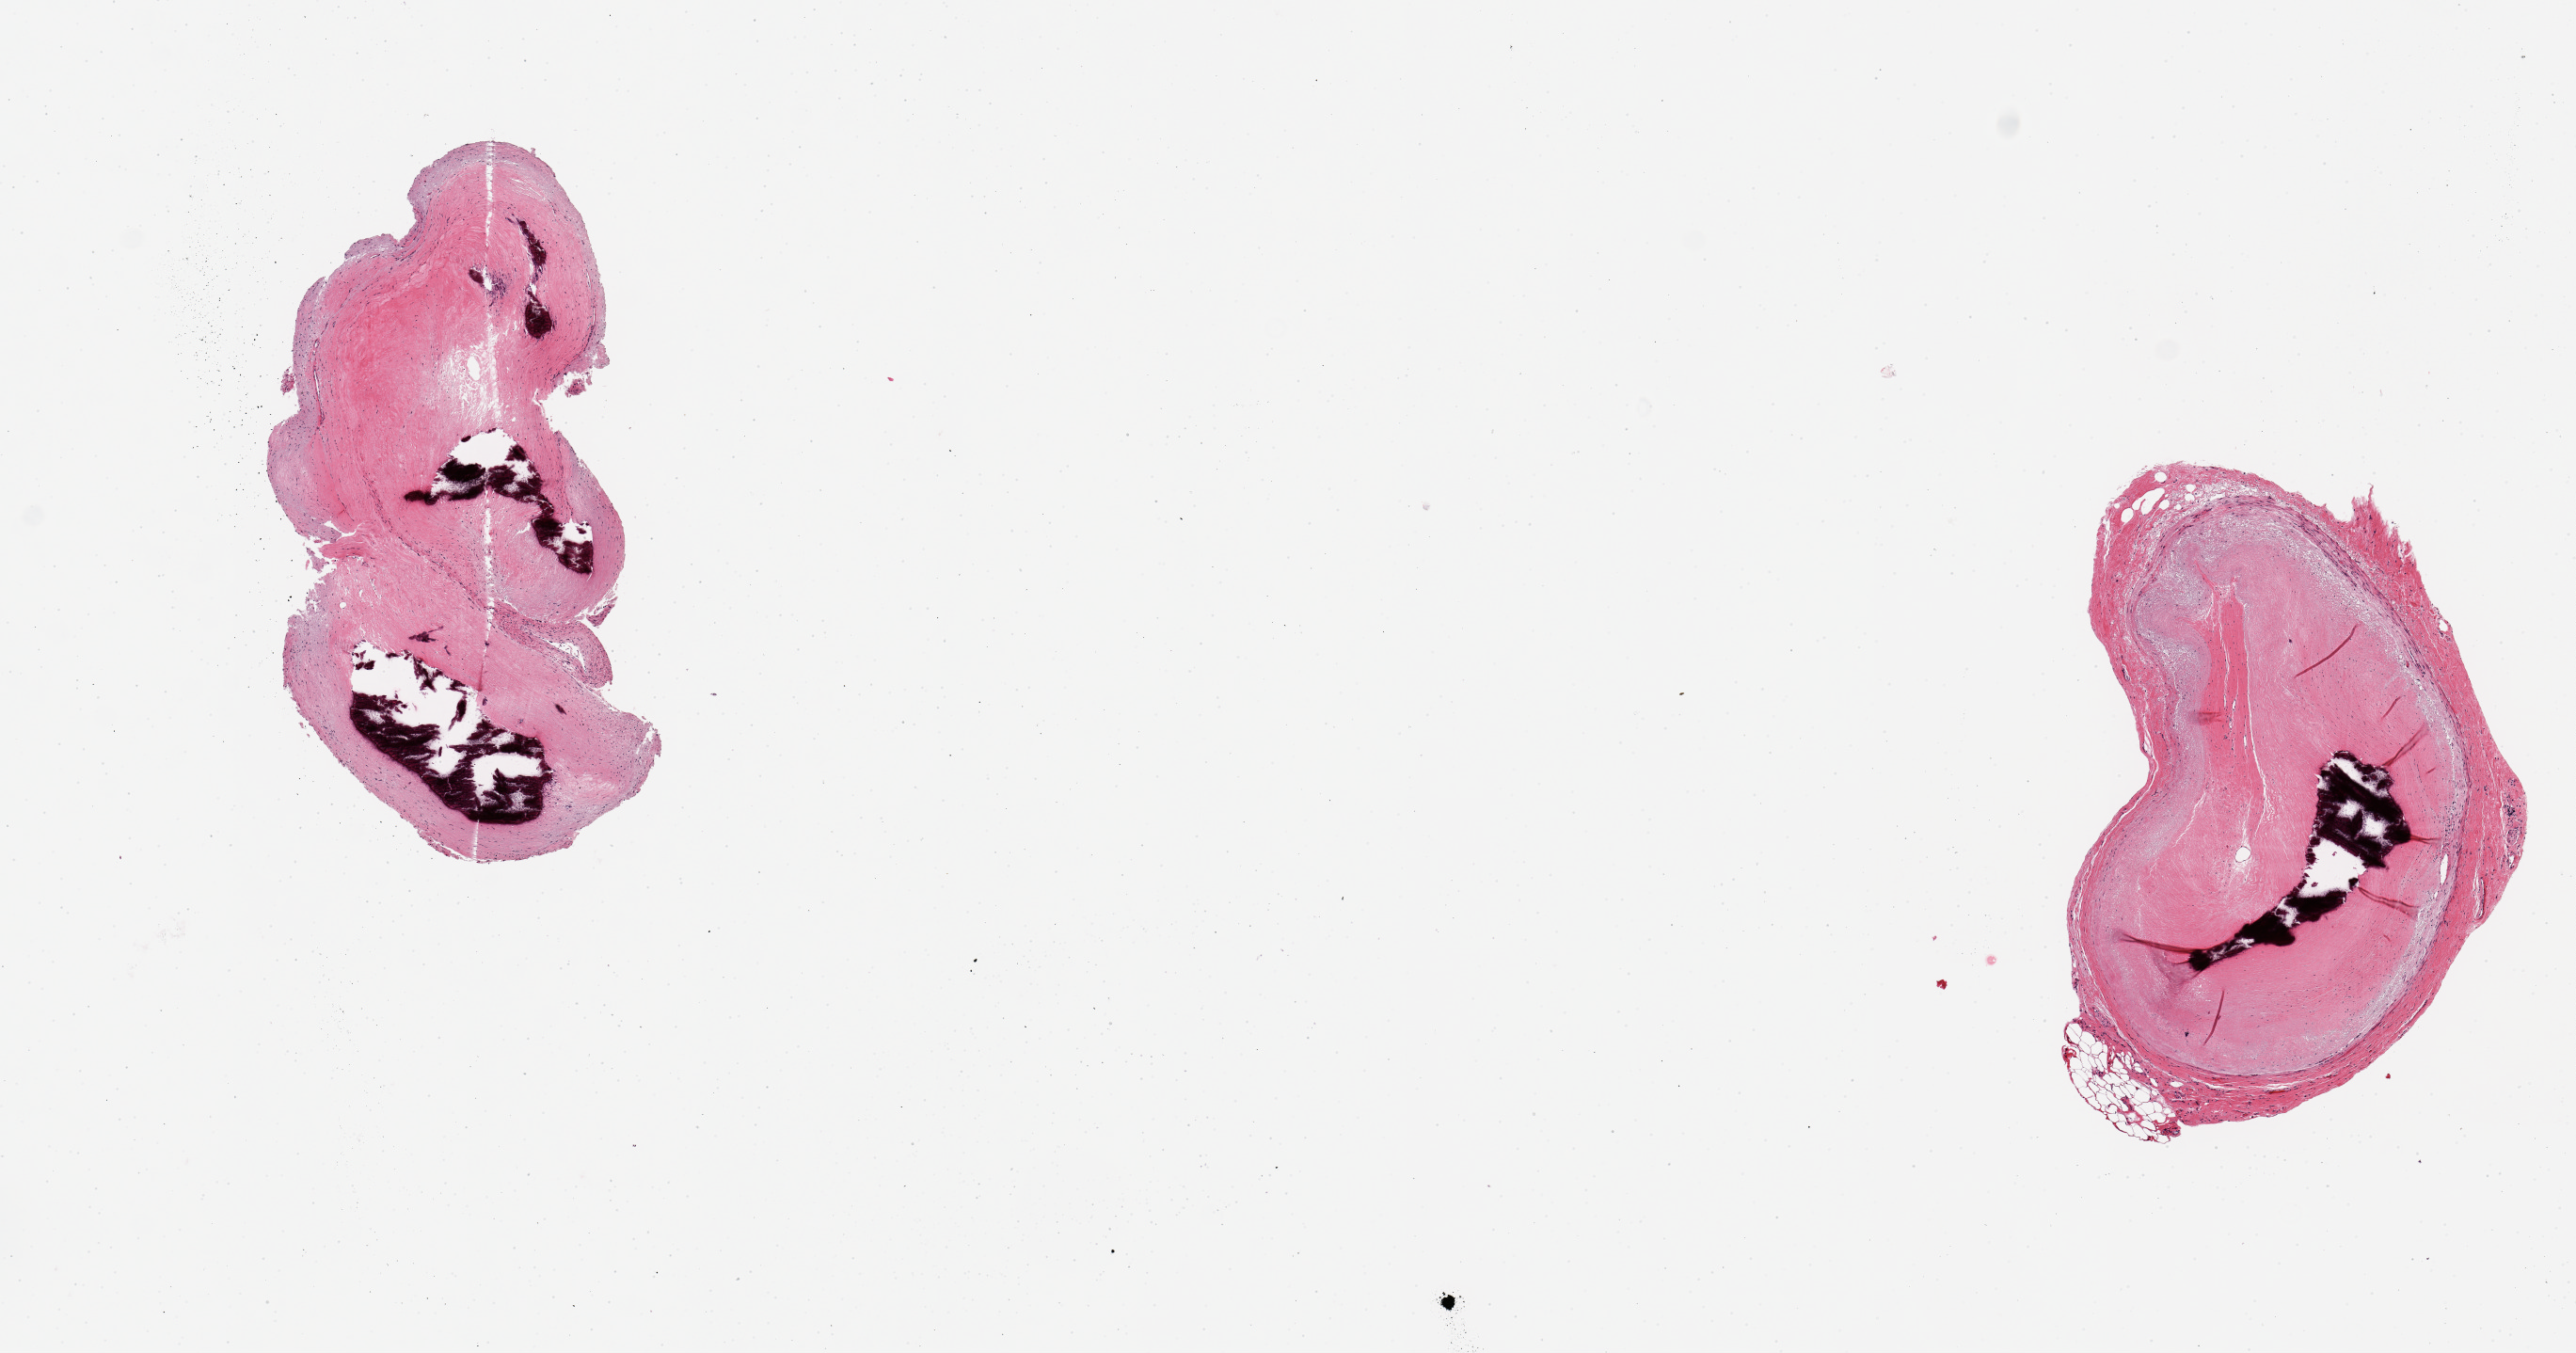
Digitized haematoxylin and eosin-stained section, brightfield, whole scanned area (about 10.8 x 5.7 mm, from a 20x scan) shown as a low-resolution overview, PAXgene-fixed paraffin-embedded (PFPE) section, target tissue: coronary artery, tissue donor sample. Donor sex: male.
Reviewer comment on this tissue sample: 2 pieces; large calcified plaques.